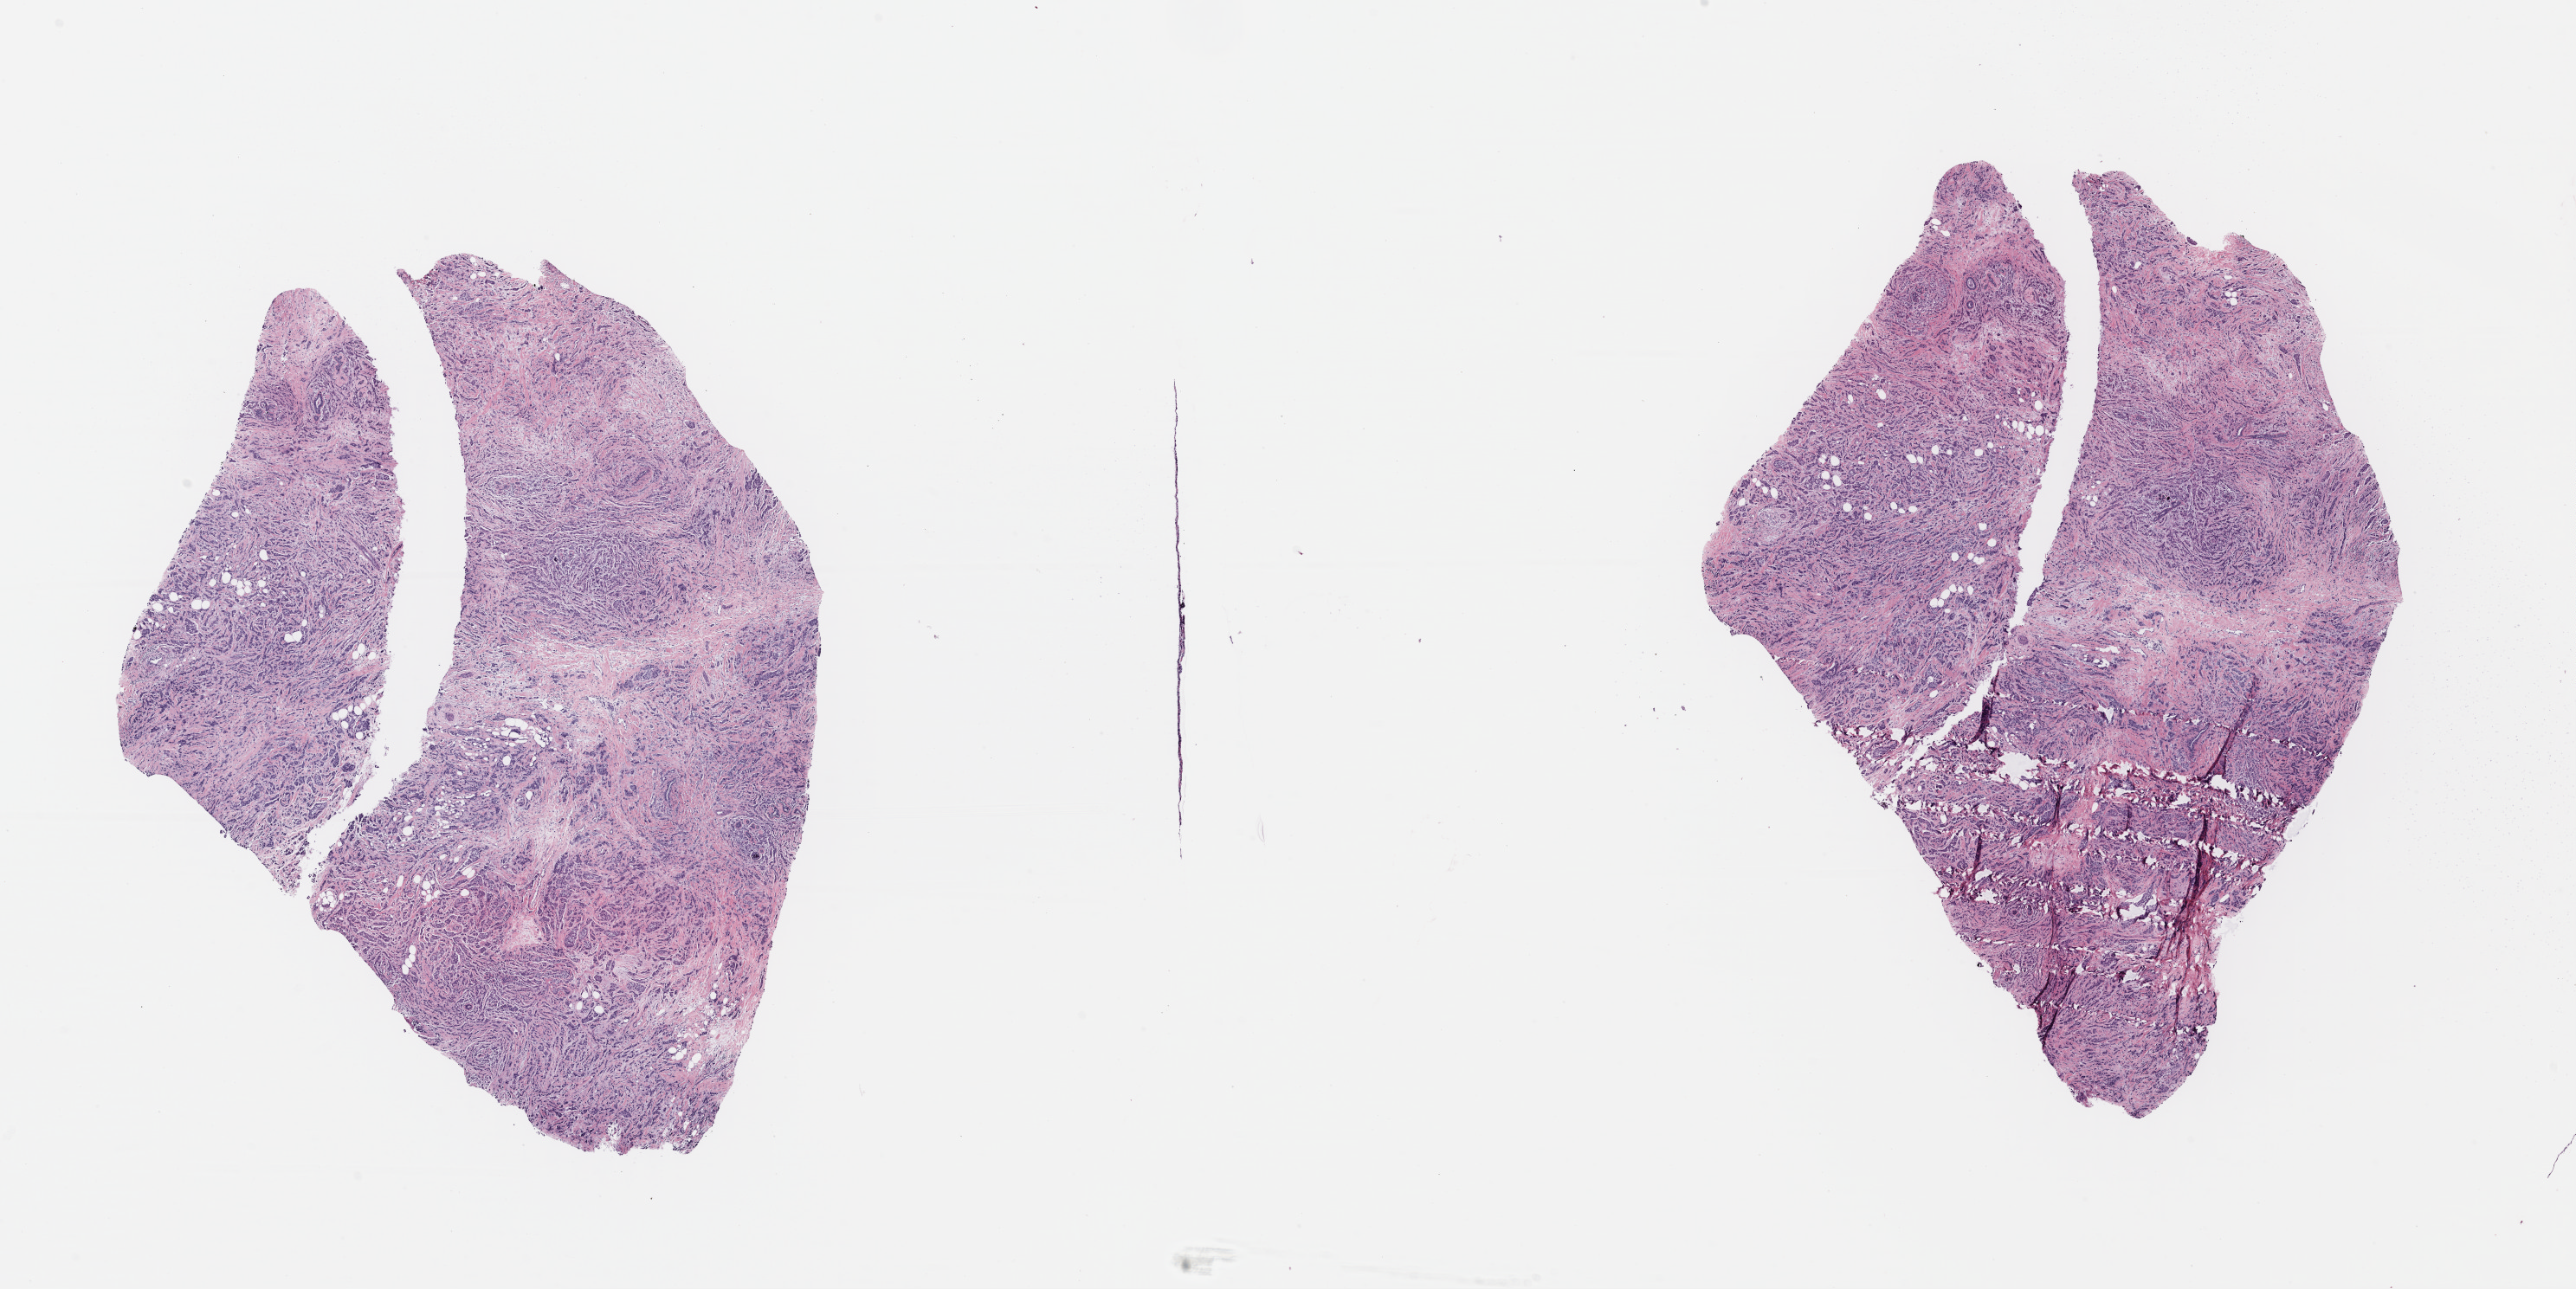
Digitized H&E-stained tissue section (whole slide), a low-resolution overview of the entire scanned area, about 23.4 x 11.7 mm, formalin-fixed paraffin-embedded (FFPE) diagnostic section, sample: primary tumour, breast. Female patient; age at initial diagnosis 44 years.
Histologic diagnosis: Infiltrating duct carcinoma, NOS.